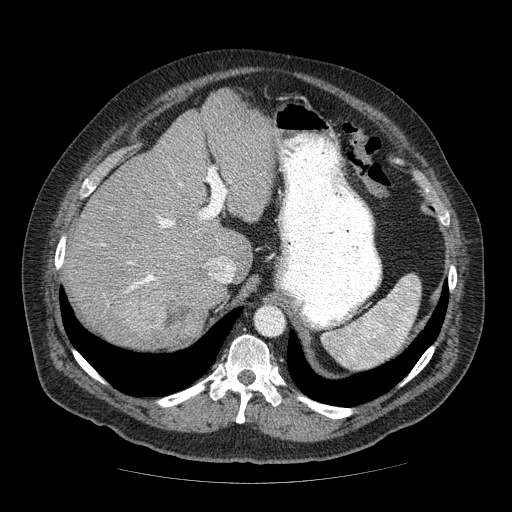
Contrast-enhanced abdominal CT (liver protocol), one axial slice; position 45 of 85 along the scan axis; reconstruction kernel STANDARD; 120 kVp; soft-tissue window (W 400 / L 40 HU); 512 × 512 image matrix, field of view 420 × 420 mm. Case-level facts recorded for this patient, not image findings: diagnosis: hepatocellular carcinoma (patient treated with transarterial chemoembolisation; whether this scan precedes or follows treatment is not stated here); TNM stage (as recorded): Stage-IIIA; Child-Pugh class: A; tumour size: 7 cm.
Structures marked on this image (semi-automatically segmented with operator editing):
- liver parenchyma outside the tumour (the mass and vessels are separate outlines, so this box may not span the whole liver): bounding box (x1, y1, x2, y2) in pixels: (66, 90, 276, 346)
- mass: (117, 279, 222, 349)
- liver vessels: (102, 183, 182, 291)